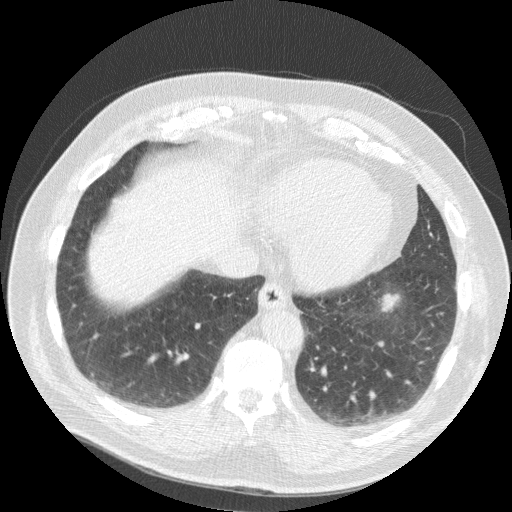
Low-dose screening chest CT, axial slice; second screening round (one year after baseline); lung window (W 1500 / L -600 HU); 2.5 mm slice thickness. Male participant, aged 63 years at enrolment. Current smoker at enrolment.
- Expert reader's lesion annotation, bounding box <362,283,410,324> (left, top, right, bottom; pixels).
- The screening reader recorded 2 non-calcified nodules or masses ≥4 mm on this exam (right middle lobe, left lower lobe); which of them this box marks is not recorded.
- Official screen result: positive, change unspecified: nodule(s) >= 4 mm or enlarging nodule(s), mass(es), or other non-specific abnormalities suspicious for lung cancer.
- Participant outcome: lung cancer diagnosed 633 days after this screen (after the third annual screen) — squamous cell carcinoma, NOS, left lower lobe, stage IB (AJCC 6th edition), 48 mm at pathology.